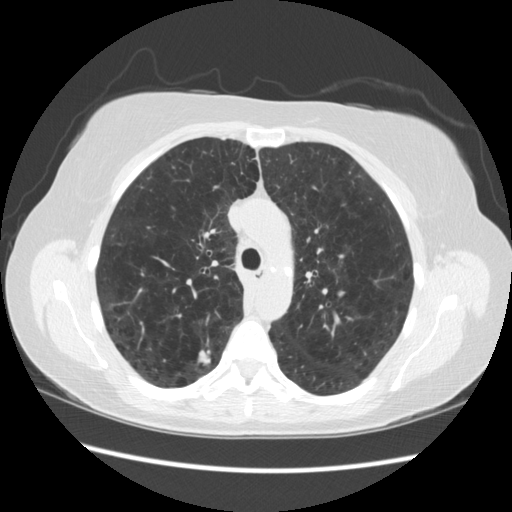
Axial slice from a low-dose chest CT screening exam. Third annual screen. Lung window (W 1500 / L -600 HU). 2.5 mm slice thickness. Slice 71 of 235 in the series. 512 × 512 image matrix, field of view 360 × 360 mm. Female, age 55 years at enrolment. Current smoker at enrolment.
Expert-annotated lung lesion, bounding box [x1, y1, x2, y2] px = [184, 336, 228, 374]. Reader record for this screening exam (exam-level; its link to the box is not recorded): non-calcified nodule or mass ≥4 mm, right upper lobe, 11 × 11 mm, poorly defined margins, soft tissue attenuation, pre-existing on the prior screen: no. Lung cancer was diagnosed 96 days after this screen: small cell carcinoma, NOS, right upper lobe.